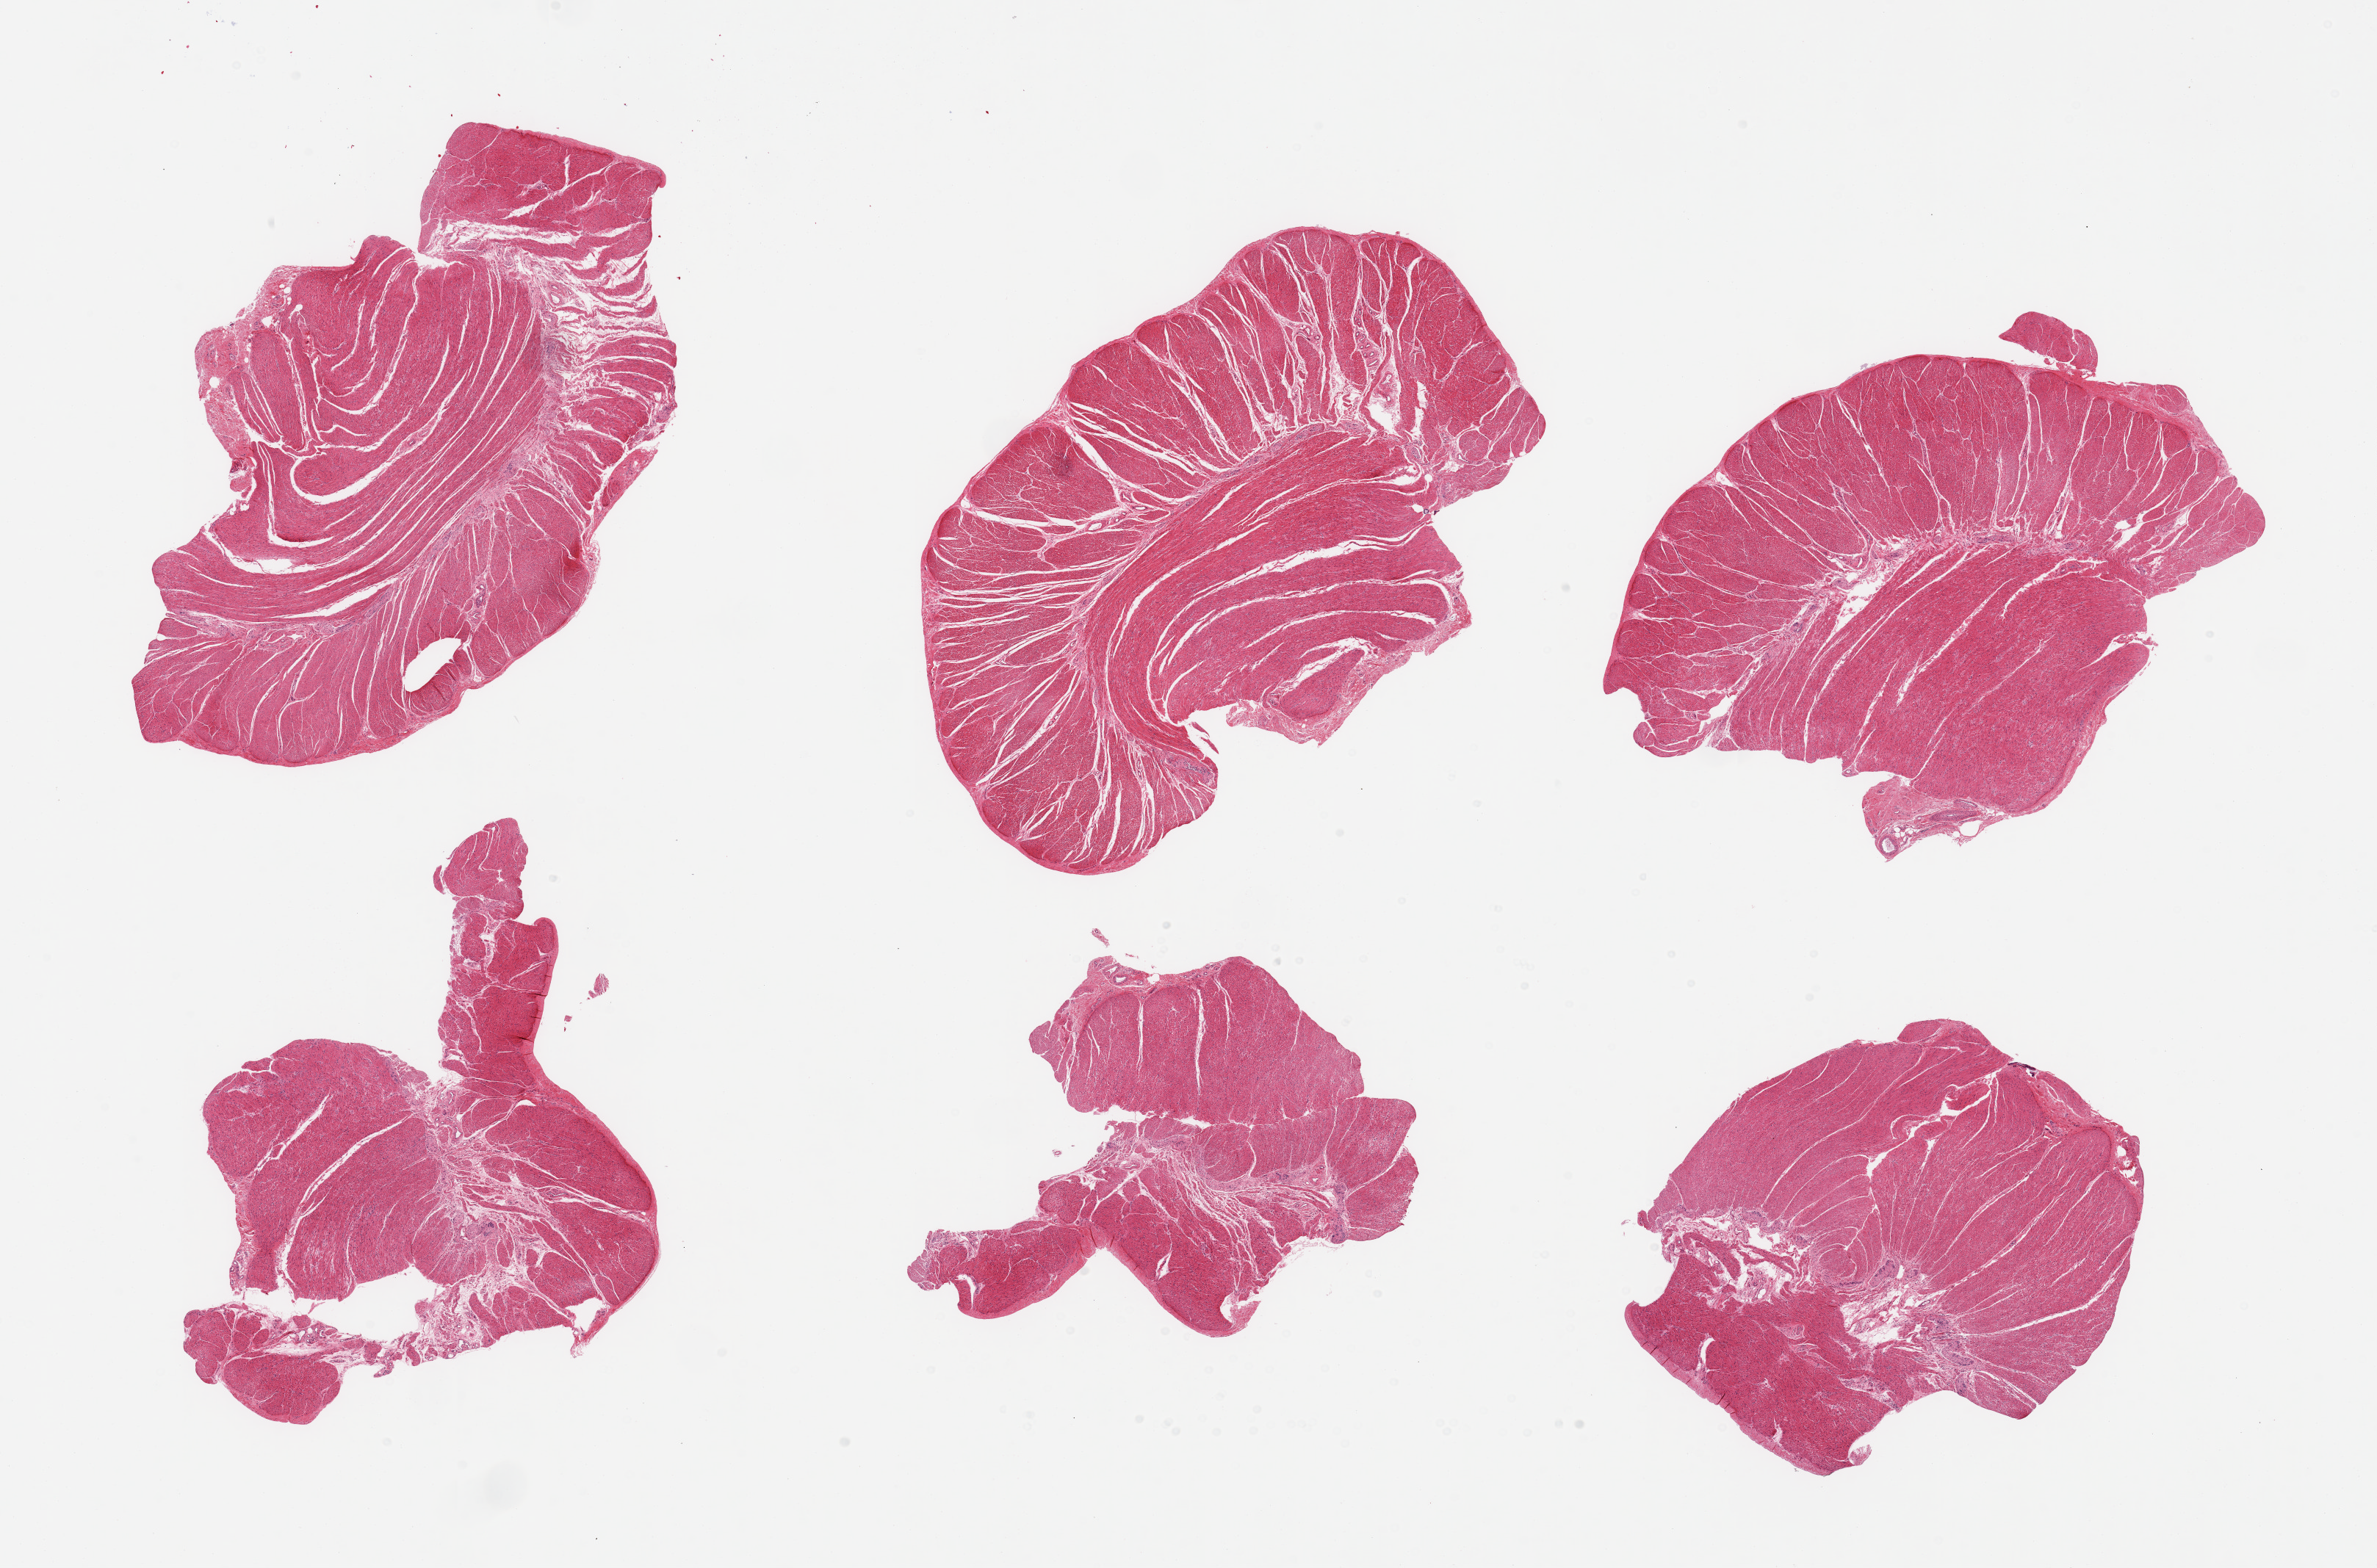
H&E whole-slide image, shown as a low-resolution overview of the whole scanned area (about 25.6 x 16.9 mm, acquisition: 20x scan), PAXgene-fixed, paraffin-embedded tissue, sampled site (target tissue): sigmoid colon, donor tissue sample.
Reviewer comment on this tissue sample: 6 pieces; well trimmed muscularis propria.